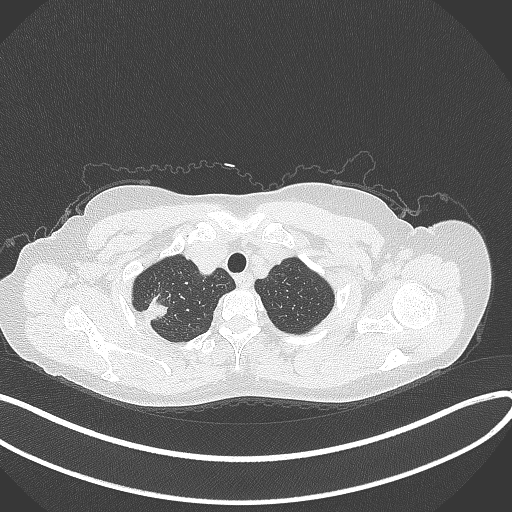
Chest CT, one axial slice; position 323 of 337 along the scan axis; 120 kVp; lung window (W 1500 / L -600 HU); 1 mm slice thickness; 512 × 512 image matrix, field of view 400 × 400 mm. Patient: female, 50 years. From the clinical record (not read from this slice): clinical TNM (as recorded): T1c N0 M0; histopathological grade: G2-3.
Annotated regions visible in this slice (bounding box drawn by a radiologist):
- lung tumour (recorded histology: adenocarcinoma): bounding box [x1, y1, x2, y2] px = [141, 291, 172, 324]